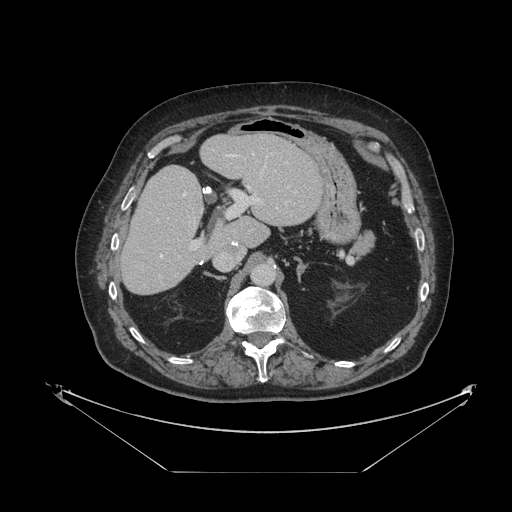
Contrast-enhanced abdominal CT, one axial slice; slice 63 of 121 in the series (ordered by position); reconstruction kernel STANDARD; 120 kVp; intravenous contrast given; soft-tissue window (W 400 / L 40 HU); 2.5 mm slice thickness; 512 × 512 image matrix, field of view 500 × 500 mm. Male patient, age 68 years. Case-level facts recorded for this patient, not image findings: diagnosis: colorectal cancer liver metastases, imaged before liver resection; multiple liver metastases: no; largest metastasis: 4 cm; chemotherapy before resection: yes.
Outlined on this slice (manually delineated by an expert):
- hepatic veins: bounding box <160,154,289,257> (left, top, right, bottom; pixels)
- liver: <122,135,322,295>
- planned liver remnant (the part of the liver to remain after resection): <122,135,322,295>
- portal vein (with intrahepatic branches): <190,191,260,250>